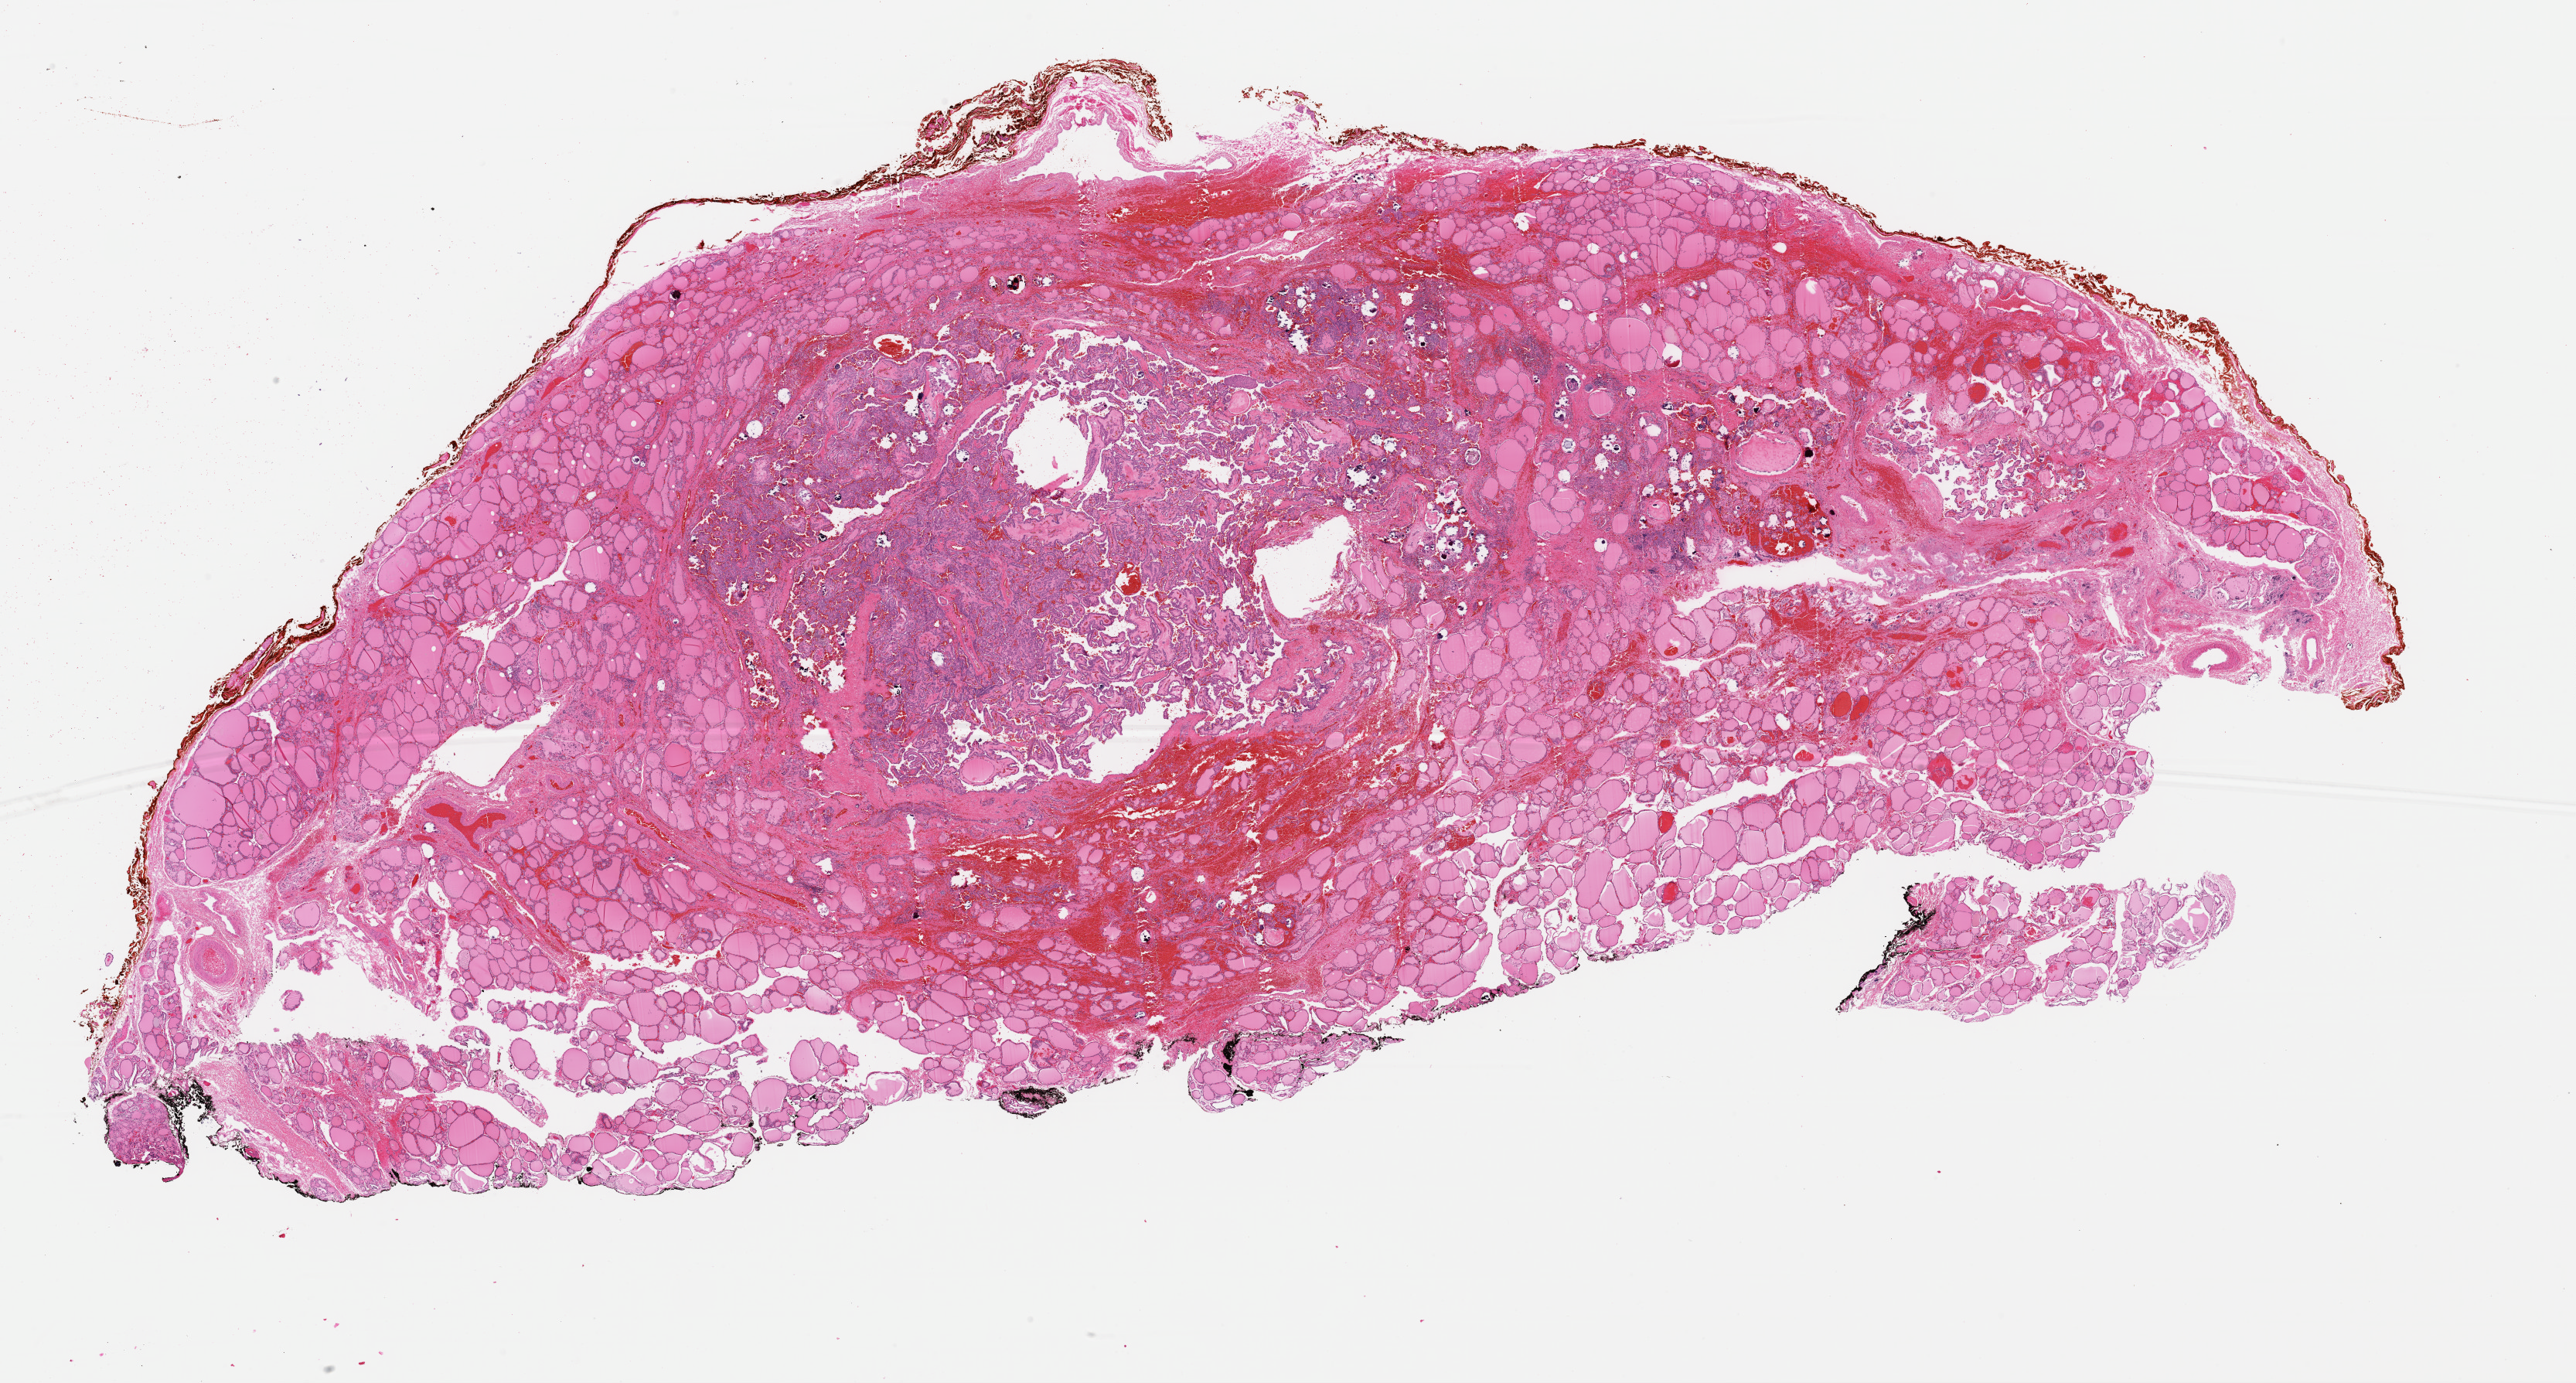
Digitized Hematoxylin and eosin (H&E) stained tissue section (whole slide), a low-resolution overview of the entire scanned area, about 26.3 x 14.1 mm; formalin-fixed paraffin-embedded (FFPE) diagnostic section; sample: primary tumour, thyroid. Female patient; age at initial diagnosis 42 years.
• laterality: left
• AJCC pathologic stage: I (6th edition)
• histologic diagnosis: Papillary adenocarcinoma, NOS